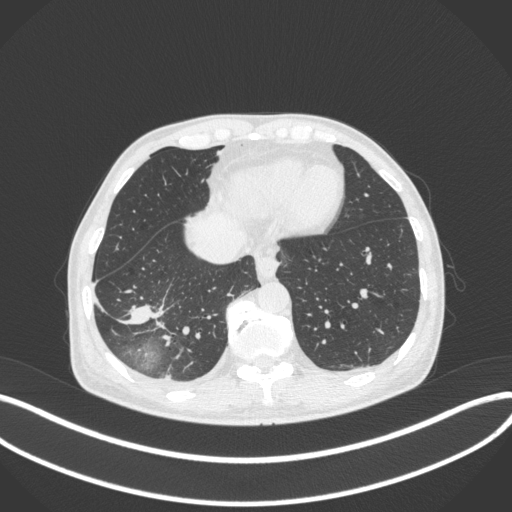
Chest CT, one axial slice; slice 96 of 385 in the series (ordered by position); 120 kVp; lung window (W 1500 / L -600 HU); 1 mm slice thickness; 512 × 512 image matrix, field of view 400 × 400 mm. Male patient, age 64 years. Case-level facts recorded for this patient, not image findings: clinical TNM (as recorded): T3 N0 M0; histopathological grade: G2-3.
Structures marked on this image (rectangle marked by the reading radiologist):
- lung tumour (recorded histology: adenocarcinoma): bounding box [x1, y1, x2, y2] px = [118, 296, 165, 328]